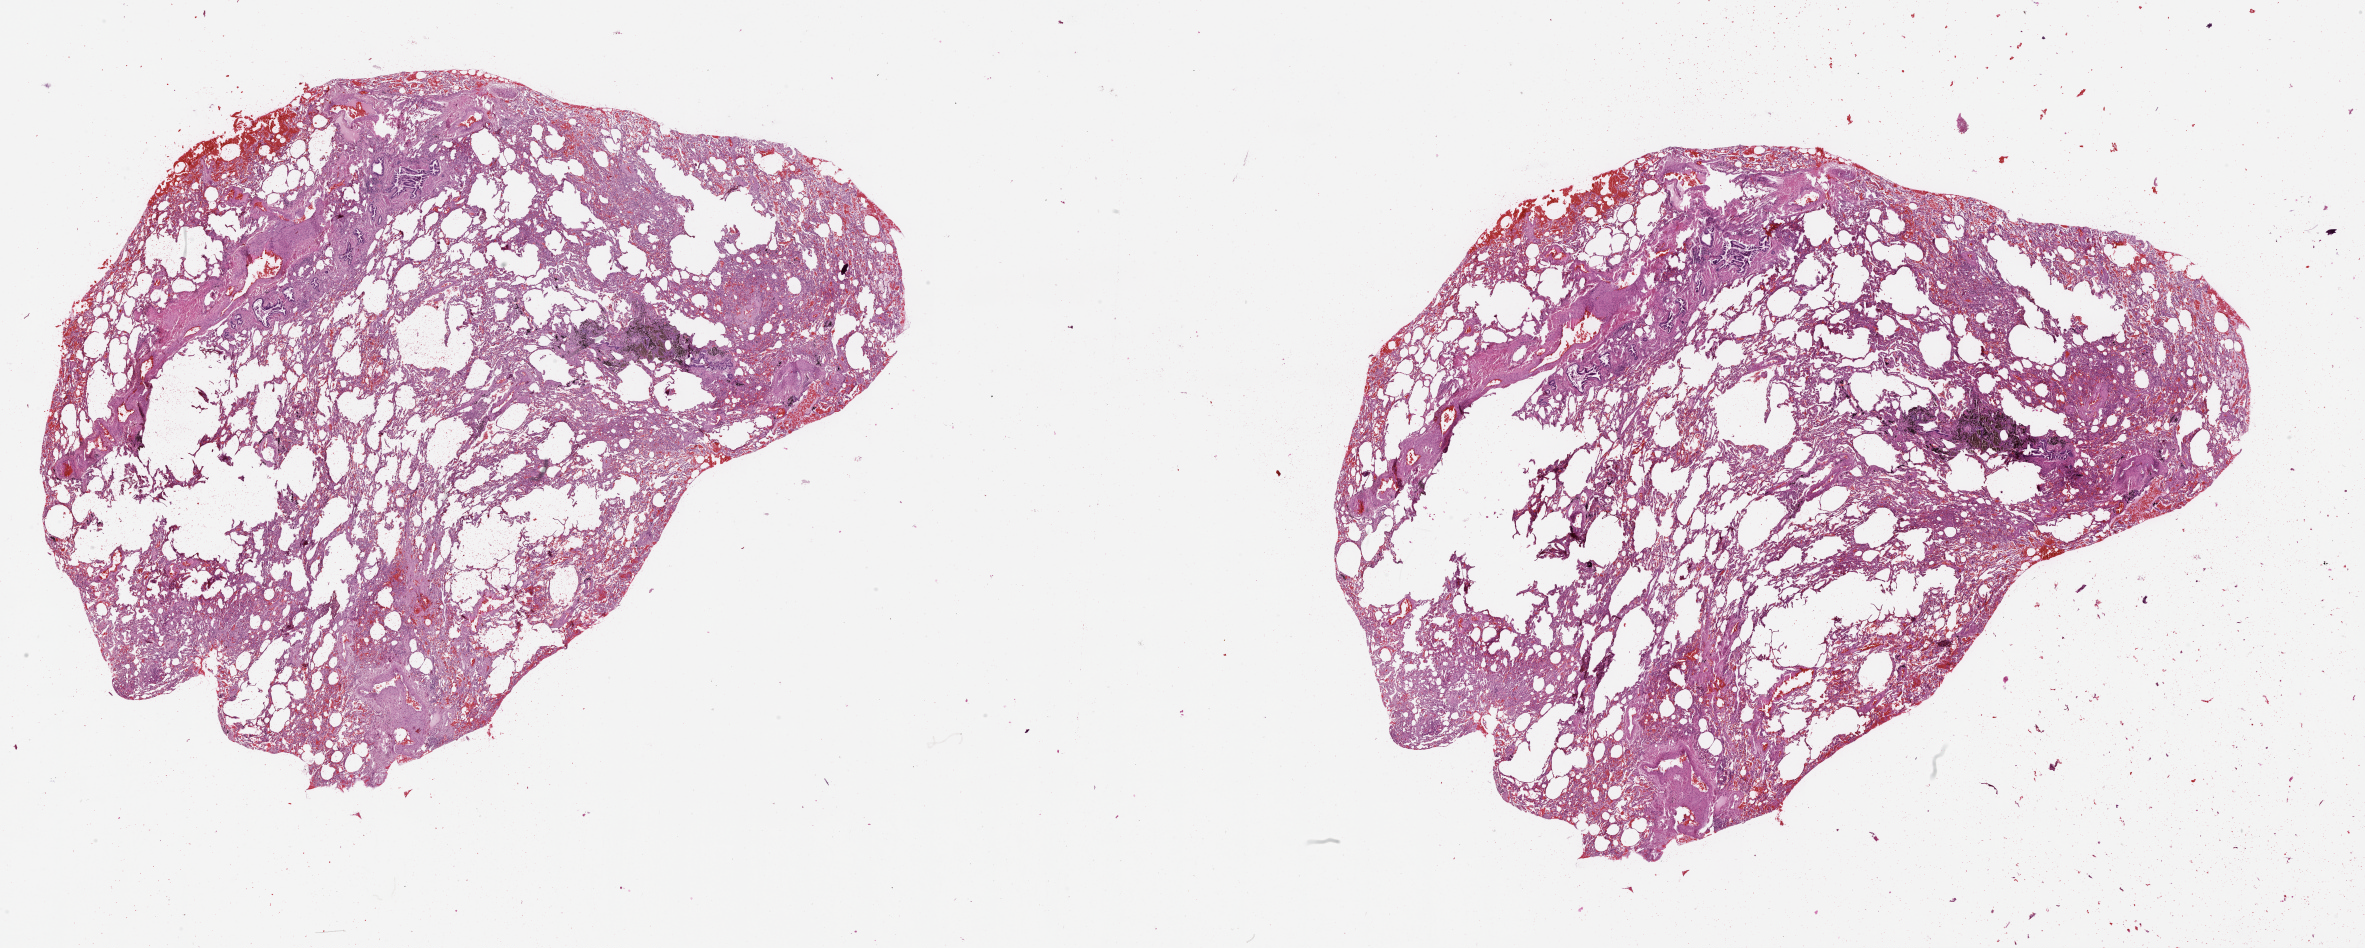
Whole-slide histology image, Hematoxylin and eosin (H&E) stained — shown as a low-resolution overview of the whole scanned area (about 38.1 x 15.3 mm, acquisition: 20x scan); lung, normal (non-tumour) tissue. Patient: male, age 58 years.
This section: normal (non-tumour) tissue from the same patient. Patient diagnosis (cohort enrolment): squamous cell carcinoma (lung).